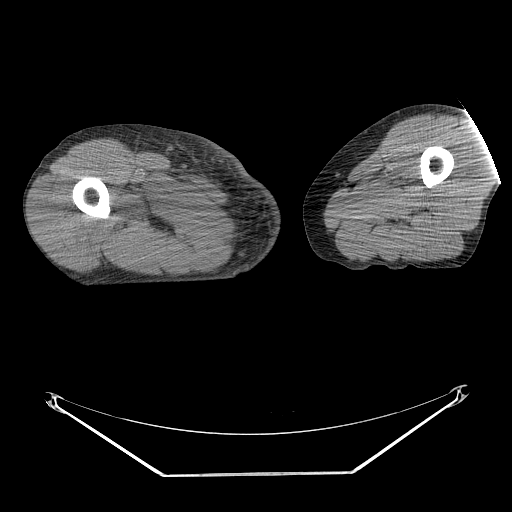
CT of an extremity soft-tissue mass (from a PET/CT study), one axial slice; slice 236 of 311 in the series (ordered by position); soft-tissue window (W 400 / L 40 HU); 3.75 mm slice thickness; 512 × 512 image matrix, field of view 500 × 500 mm. Male patient. Case-level facts recorded for this patient, not image findings: histological type: undifferentiated - pleiomorphic; grade: high; site of the primary tumour: right thigh.
Structures marked on this image (expert contour drawn on MRI and transferred to this co-registered scan by the dataset authors):
- gross tumour volume including surrounding oedema: bounding box <135,187,202,220> (left, top, right, bottom; pixels)